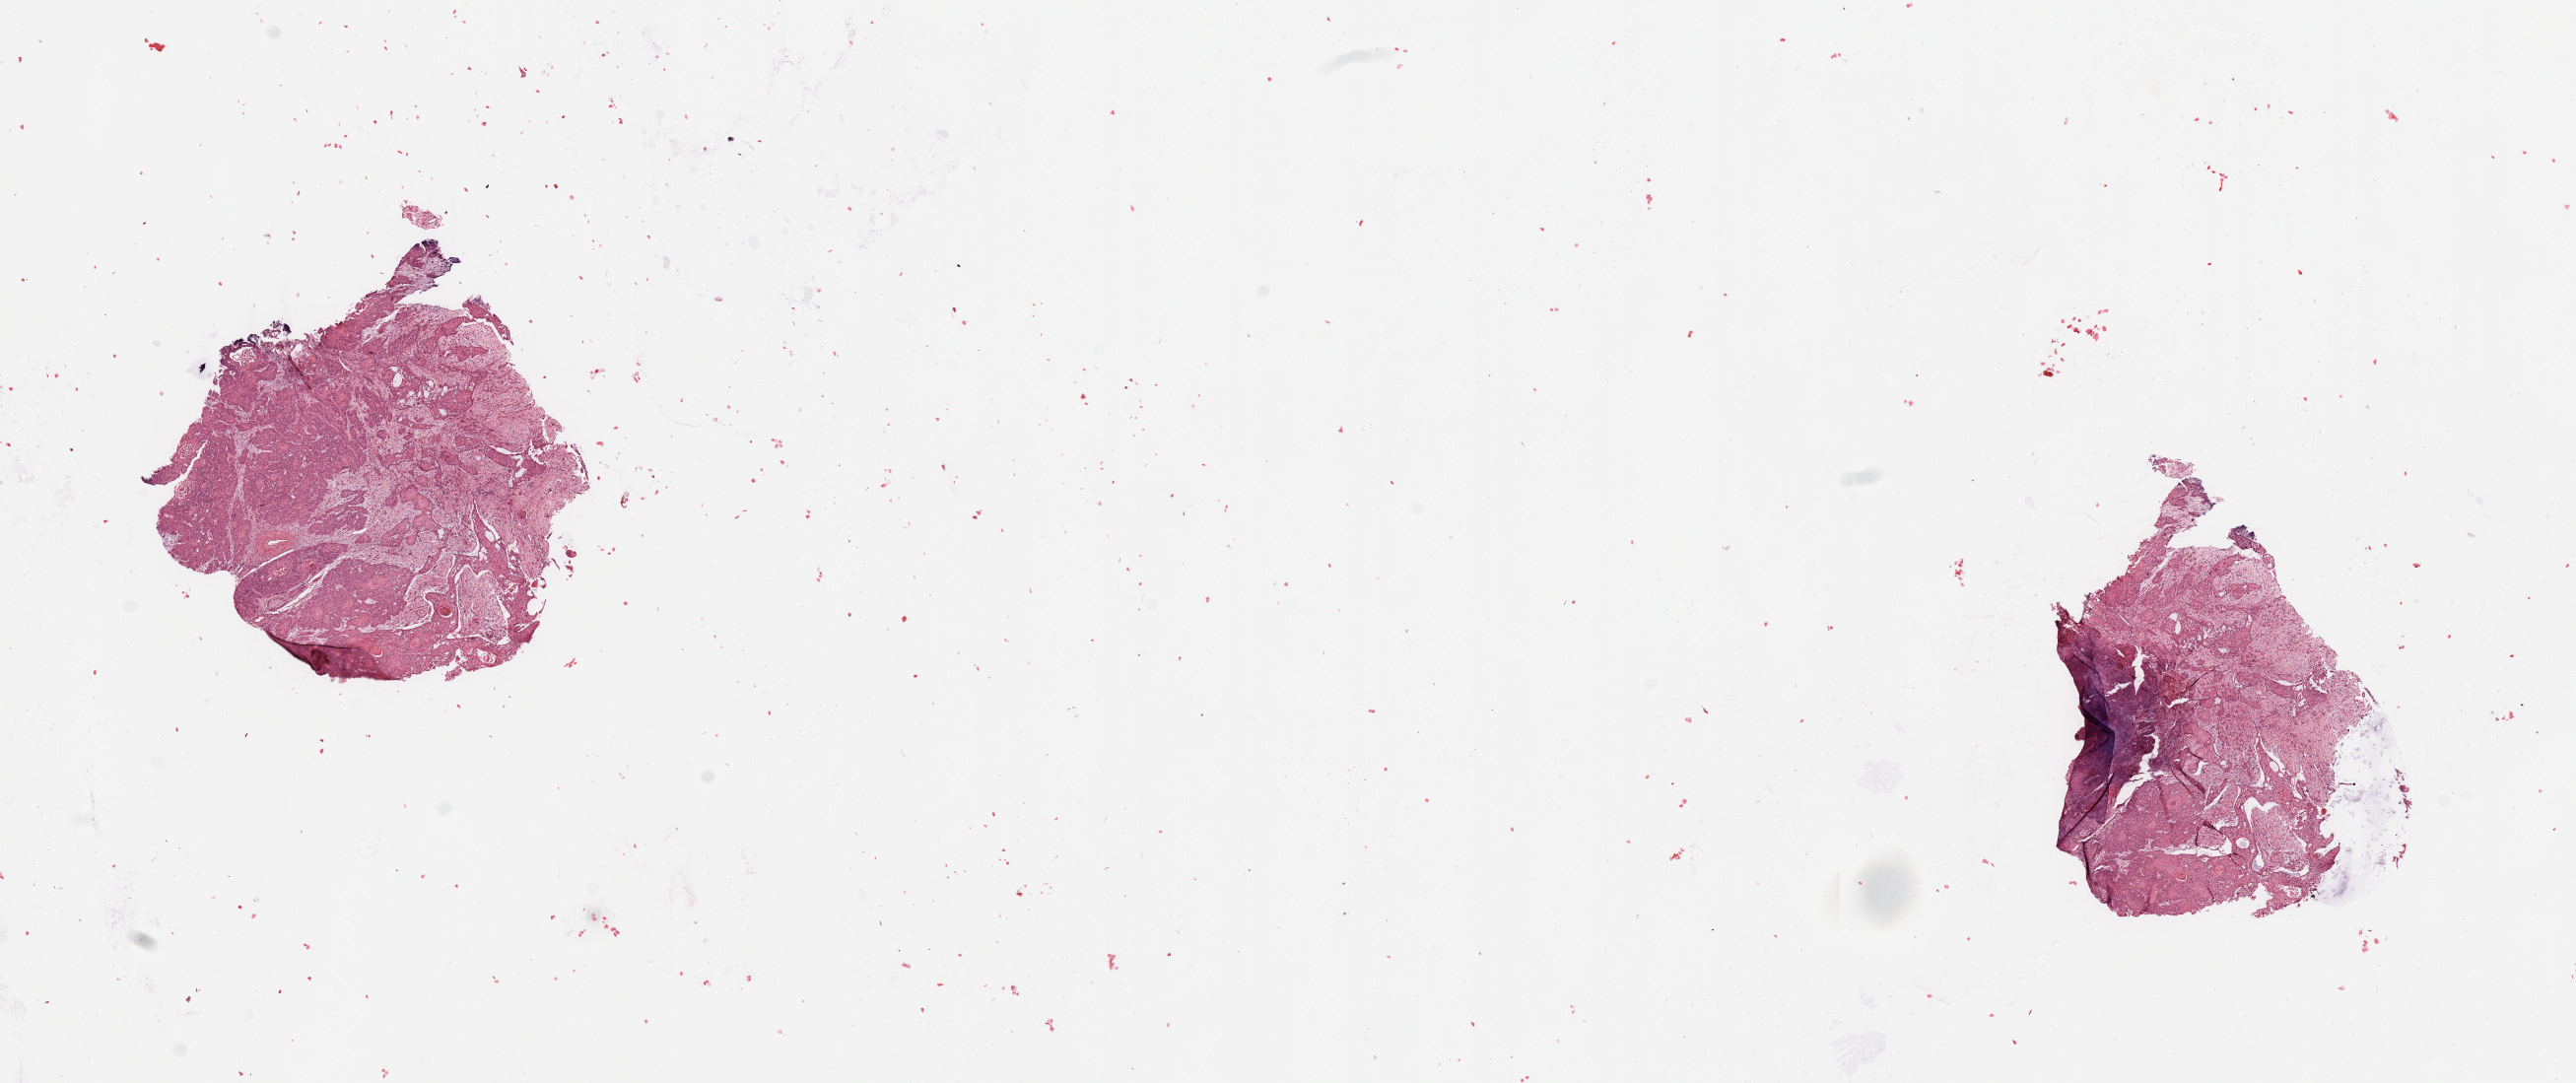
Whole-slide histology image, H&E, a low-resolution overview of the entire scanned area, about 20.7 x 8.7 mm (from a 20x scan); tumour tissue sample, sampled site: oral cavity. Male, 58 y/o. Histologic grade: G2 (moderately differentiated). Slide review estimates, as recorded: tumour nuclei 80%, necrosis 2%.
Primary tumour site (as recorded): oral cavity. AJCC pathologic stage: IVA. Histologic diagnosis: Squamous cell carcinoma, NOS (overlapping lesion of lip, oral cavity and pharynx).